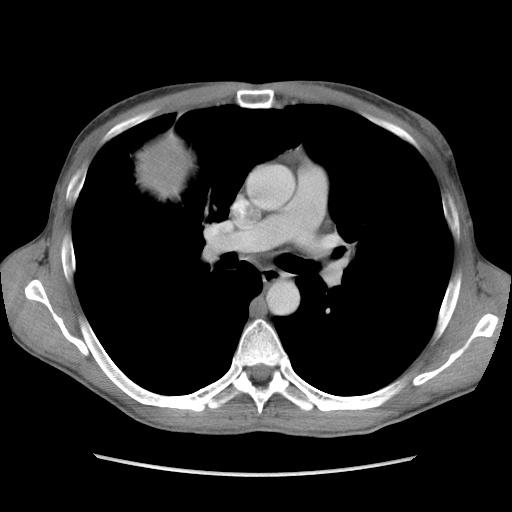
Contrast-enhanced abdominal CT, one axial slice; position 107 of 115 along the scan axis; soft-tissue window (W 400 / L 40 HU); 5 mm slice thickness; 512 × 512 image matrix, field of view 360 × 360 mm. Male patient. Case-level facts recorded for this patient, not image findings: diagnosis: adrenocortical carcinoma; tumour side: right adrenal; Ki-67 index: 13 %; stage (as recorded): 3.
Structures marked on this image (semi-automatically segmented with operator editing):
- mass: bounding box <136,138,191,194> (left, top, right, bottom; pixels)